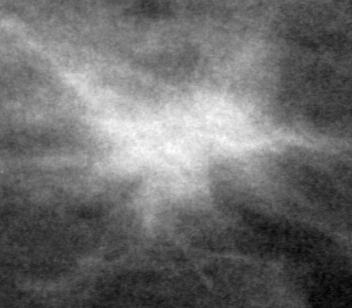
Cropped region of a digitized screen-film mammogram centred on a radiologist-marked abnormality, right breast, MLO view, BI-RADS breast density category 3 (scale 1–4).
Marked abnormality: mass, shape irregular, margins spiculated; BI-RADS assessment category 5; pathology (as recorded): malignant.